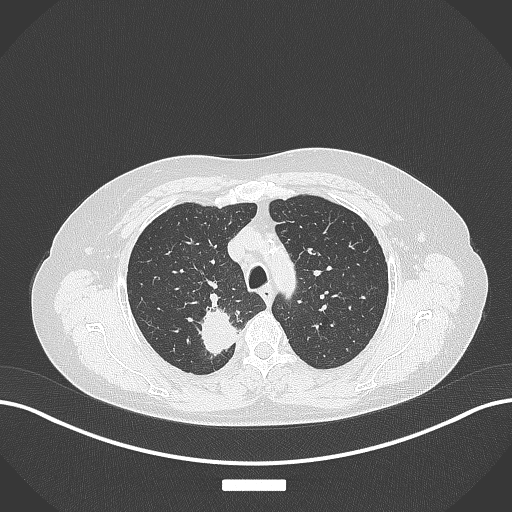
Chest CT, one axial slice; position 297 of 357 along the scan axis; 120 kVp; lung window (W 1500 / L -600 HU); 1 mm slice thickness; 512 × 512 image matrix. Patient: female, 62 years. Case-level facts recorded for this patient, not image findings: clinical TNM (as recorded): T1c N1 M0.
Outlined on this slice (bounding box drawn by a radiologist):
- lung tumour (recorded histology: squamous cell carcinoma): bounding box (x1, y1, x2, y2) in pixels: (192, 302, 236, 360)